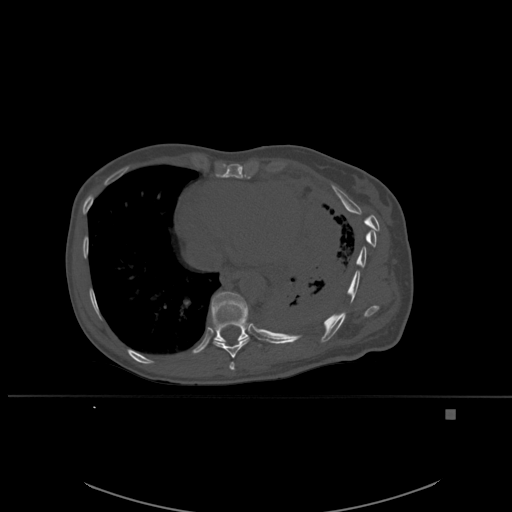
CT including the spine, one axial slice; slice 328 of 537 in the series (ordered by position); bone window (W 1800 / L 400 HU); 1.5 mm slice thickness; 512 × 512 image matrix, field of view 440 × 440 mm. Patient: female, 45 years. Case-level facts recorded for this patient, not image findings: primary cancer: lung.
Outlined on this slice (semi-automatically segmented with operator editing):
- T10 vertebra: bounding box <211,291,261,347> (left, top, right, bottom; pixels)
- T8 vertebra: <229,362,235,370>
- T9 vertebra: <213,313,250,358>